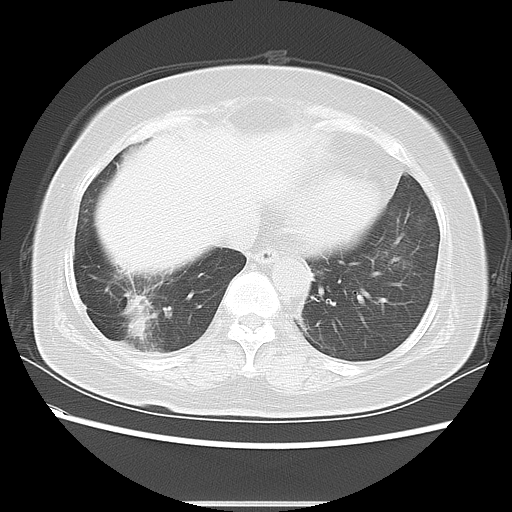
Chest CT, one axial slice. Slice 19 of 61 in the series (ordered by position). 120 kVp. Lung window (W 1500 / L -600 HU). 5 mm slice thickness. 512 × 512 image matrix, field of view 350 × 350 mm. Female patient, age 65 years. Case-level facts recorded for this patient, not image findings: clinical TNM (as recorded): T2 N0 M1b.
Annotated regions visible in this slice (rectangle marked by the reading radiologist):
- lung tumour (recorded histology: adenocarcinoma): bounding box (x1, y1, x2, y2) in pixels: (120, 287, 154, 349)